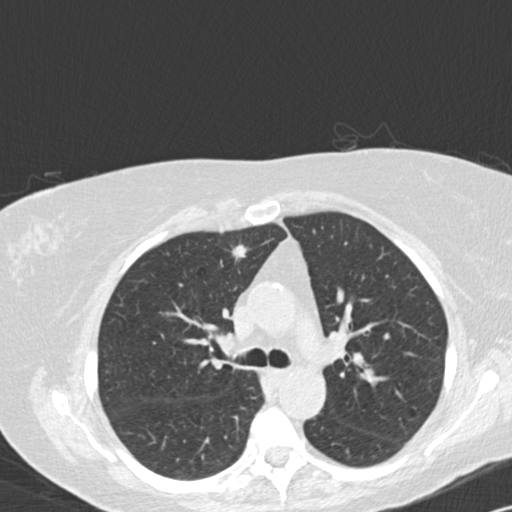
Chest CT (low-dose screening protocol), one axial image; third screening round (two years after baseline); lung window (W 1500 / L -600 HU); standard (soft-tissue) reconstruction kernel (B30f); slice 46 of 141 in the series; 512 × 512 image matrix, field of view 328 × 328 mm. Female participant, aged 72 years at enrolment.
Expert-annotated lung lesion, box from (x=216, y=233) to (x=262, y=279) px. Reader record for this screening exam (exam-level; its link to the box is not recorded): non-calcified nodule or mass ≥4 mm, right upper lobe, 8 × 8 mm, spiculated (stellate) margins, soft tissue attenuation, pre-existing on the prior screen: yes; interval growth: yes. Official screen result: positive, other. Lung cancer was diagnosed 154 days after this screen: adenocarcinoma, NOS, right upper lobe, moderately differentiated (G2), stage IA (AJCC 6th edition), 15 mm at pathology.